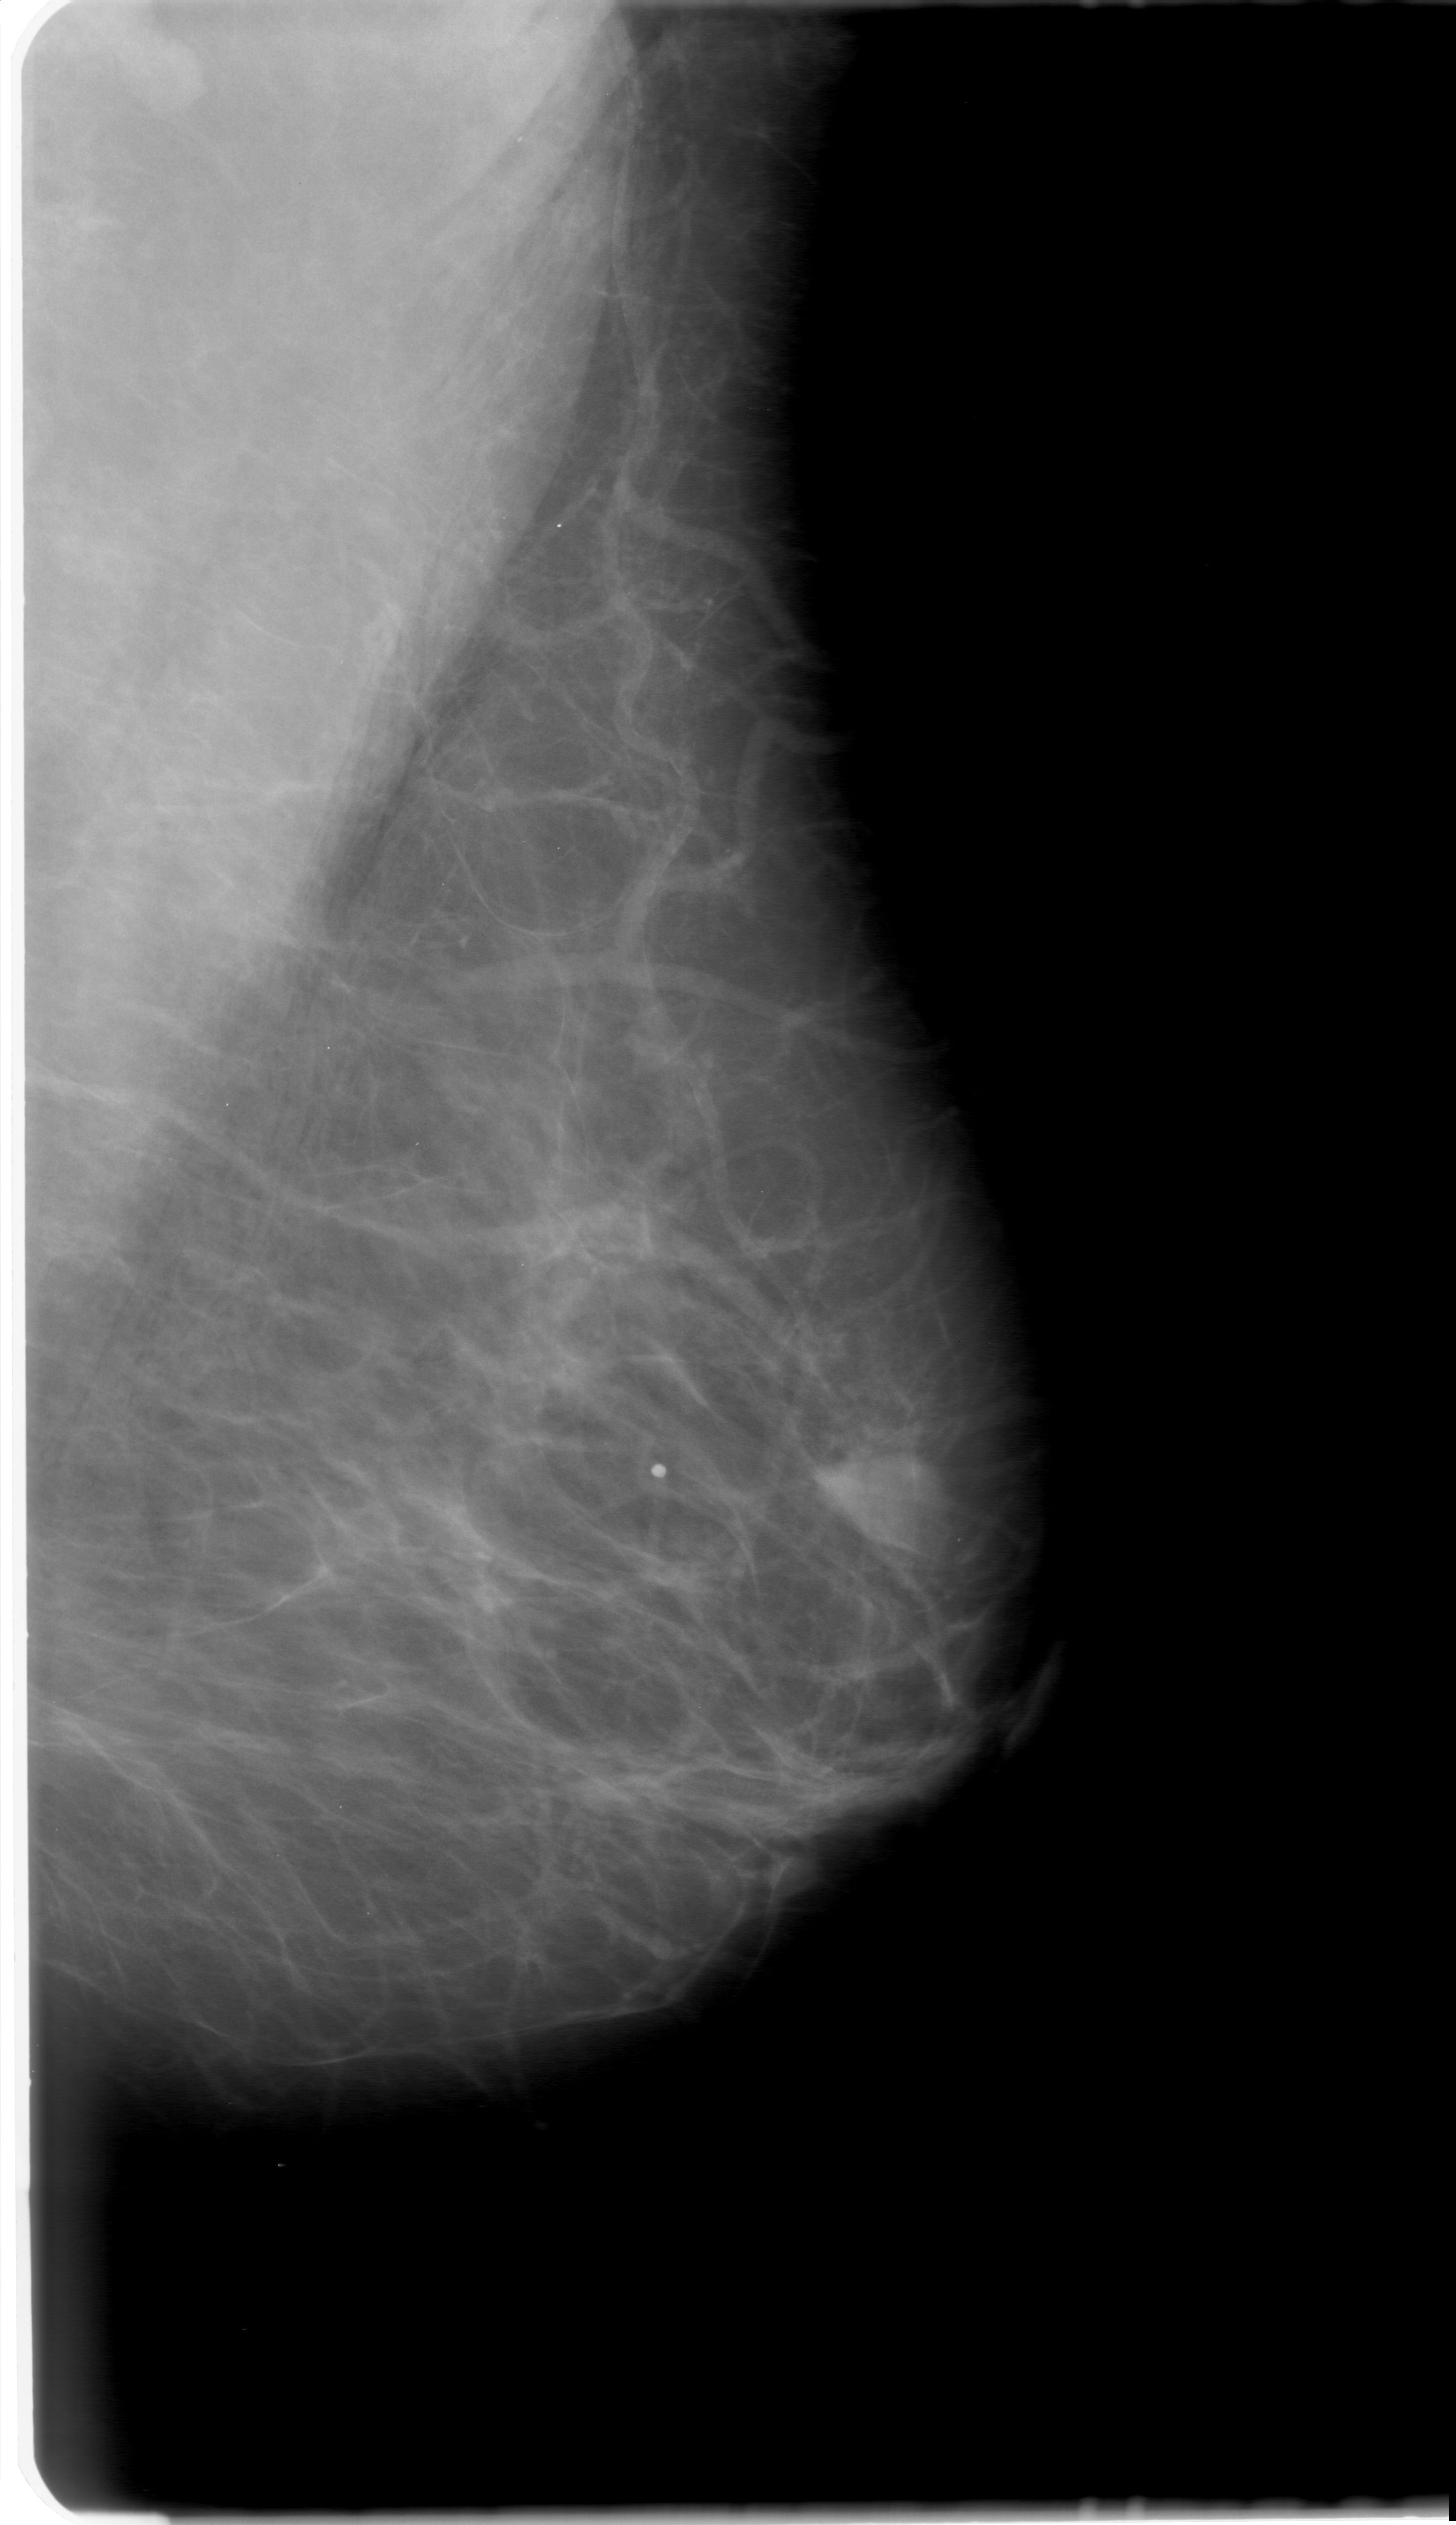
Digitized screen-film mammogram; left breast; mediolateral oblique (MLO) view; breast composition: almost entirely fatty (BI-RADS density category 1 of 4).
Mass, shape lobulated, margins obscured; BI-RADS assessment category 0; pathology result (as recorded, not read from the image): benign.